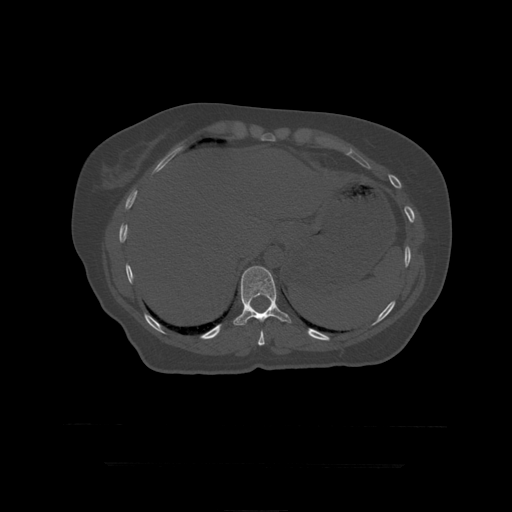
CT including the spine, one axial slice. Position 223 of 399 along the scan axis. Reconstruction kernel STANDARD. 120 kVp. Bone window (W 1800 / L 400 HU). 1.25 mm slice thickness. 512 × 512 image matrix, field of view 450 × 450 mm. Patient age 41 years. From the clinical record (not read from this slice): primary cancer: breast.
Annotated regions visible in this slice (semi-automatically segmented with operator editing):
- T10 vertebra: bounding box <258,330,265,346> (left, top, right, bottom; pixels)
- T11 vertebra: <233,266,292,326>